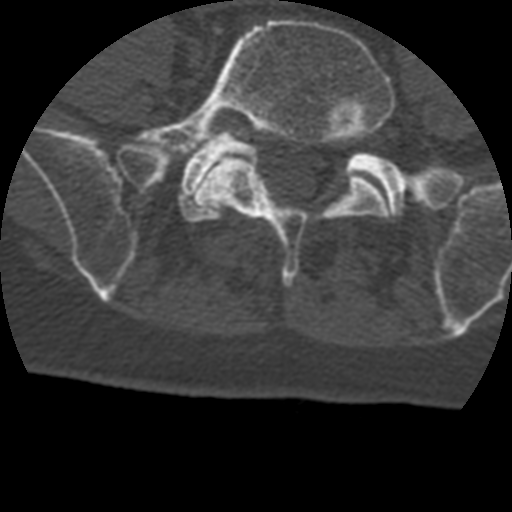
CT including the spine, one axial slice. Slice 38 of 399 in the series (ordered by position). Reconstruction kernel STANDARD. Bone window (W 1800 / L 400 HU). 1.25 mm slice thickness. 512 × 512 image matrix, field of view 160 × 160 mm. Patient age 69 years. Case-level facts recorded for this patient, not image findings: primary cancer: prostate.
Annotated regions visible in this slice (semi-automatic segmentation, software-assisted and operator-edited):
- L5 vertebra: box from (x=135, y=19) to (x=395, y=287) px